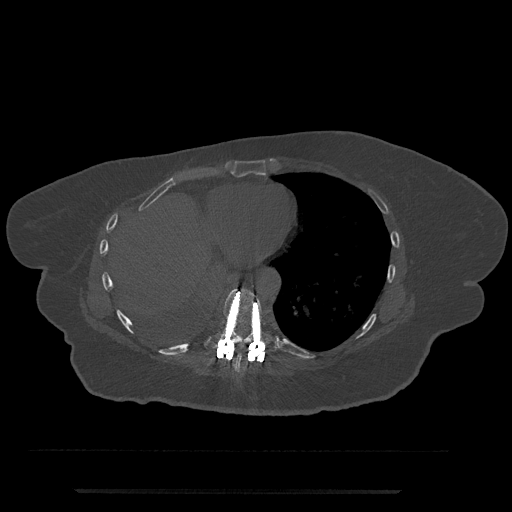
CT including the spine, one axial slice. Position 349 of 797 along the scan axis. 120 kVp. Bone window (W 1800 / L 400 HU). 0.5 mm slice thickness. 512 × 512 image matrix. Patient: female, 51 years. Case-level facts recorded for this patient, not image findings: primary cancer: neuro; vertebrae with lytic lesions (as recorded): T8.
Outlined on this slice (semi-automatically segmented with operator editing):
- T8 vertebra: bounding box [x1, y1, x2, y2] px = [233, 343, 251, 374]
- T9 vertebra: [205, 288, 277, 362]